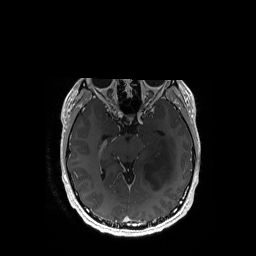
Brain MRI from a brain-tumour surgery series, one axial slice; slice 103 of 192 in the series (ordered by position); T1-weighted post-contrast; 256 × 256 image matrix, field of view 256 × 256 mm. Case-level facts recorded for this patient, not image findings: histopathology: Astrocytoma; WHO grade: 3; IDH mutation: yes; tumour location: Left Temporal.
Structures marked on this image (outlined manually by an expert reader):
- tumour: bounding box <143,134,176,190> (left, top, right, bottom; pixels)